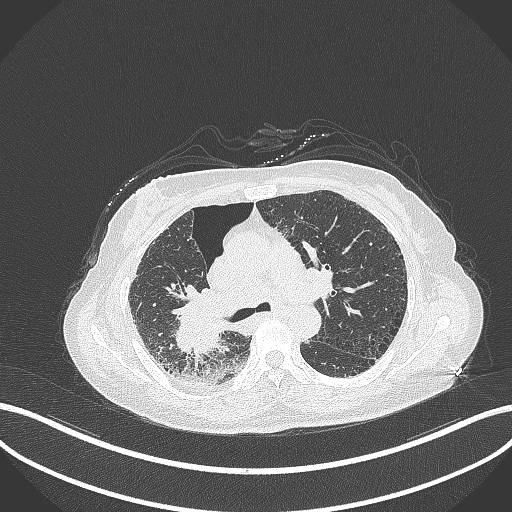
Chest CT, one axial slice; slice 220 of 408 in the series (ordered by position); 120 kVp; lung window (W 1500 / L -600 HU); 512 × 512 image matrix, field of view 400 × 400 mm. Female patient, age 64 years. From the clinical record (not read from this slice): clinical TNM (as recorded): T3 N3 M0.
Structures marked on this image (bounding box drawn by a radiologist):
- lung tumour (recorded histology: squamous cell carcinoma): box from (x=165, y=285) to (x=233, y=359) px